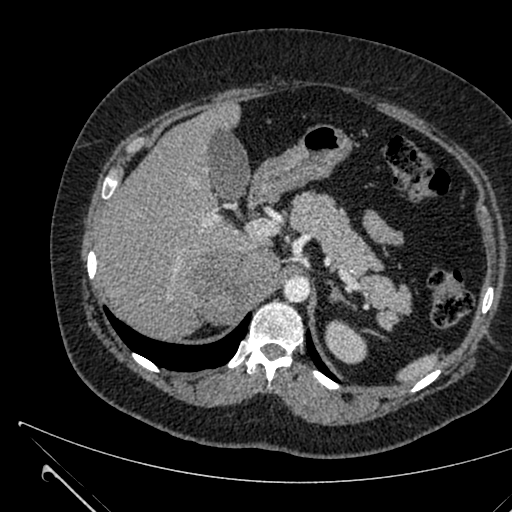
Contrast-enhanced abdominal CT, one axial slice. Slice 454 of 731 in the series (ordered by position). Intravenous contrast given. Soft-tissue window (W 400 / L 40 HU). 512 × 512 image matrix, field of view 376 × 376 mm. Patient: female, 36 years. From the clinical record (not read from this slice): diagnosis: adrenocortical carcinoma; tumour side: right adrenal; tumour size at pathology: 10 cm; Ki-67 index: 20 %; stage (as recorded): 4.
Annotated regions visible in this slice (semi-automatically segmented with operator editing):
- mass: box from (x=186, y=246) to (x=276, y=323) px